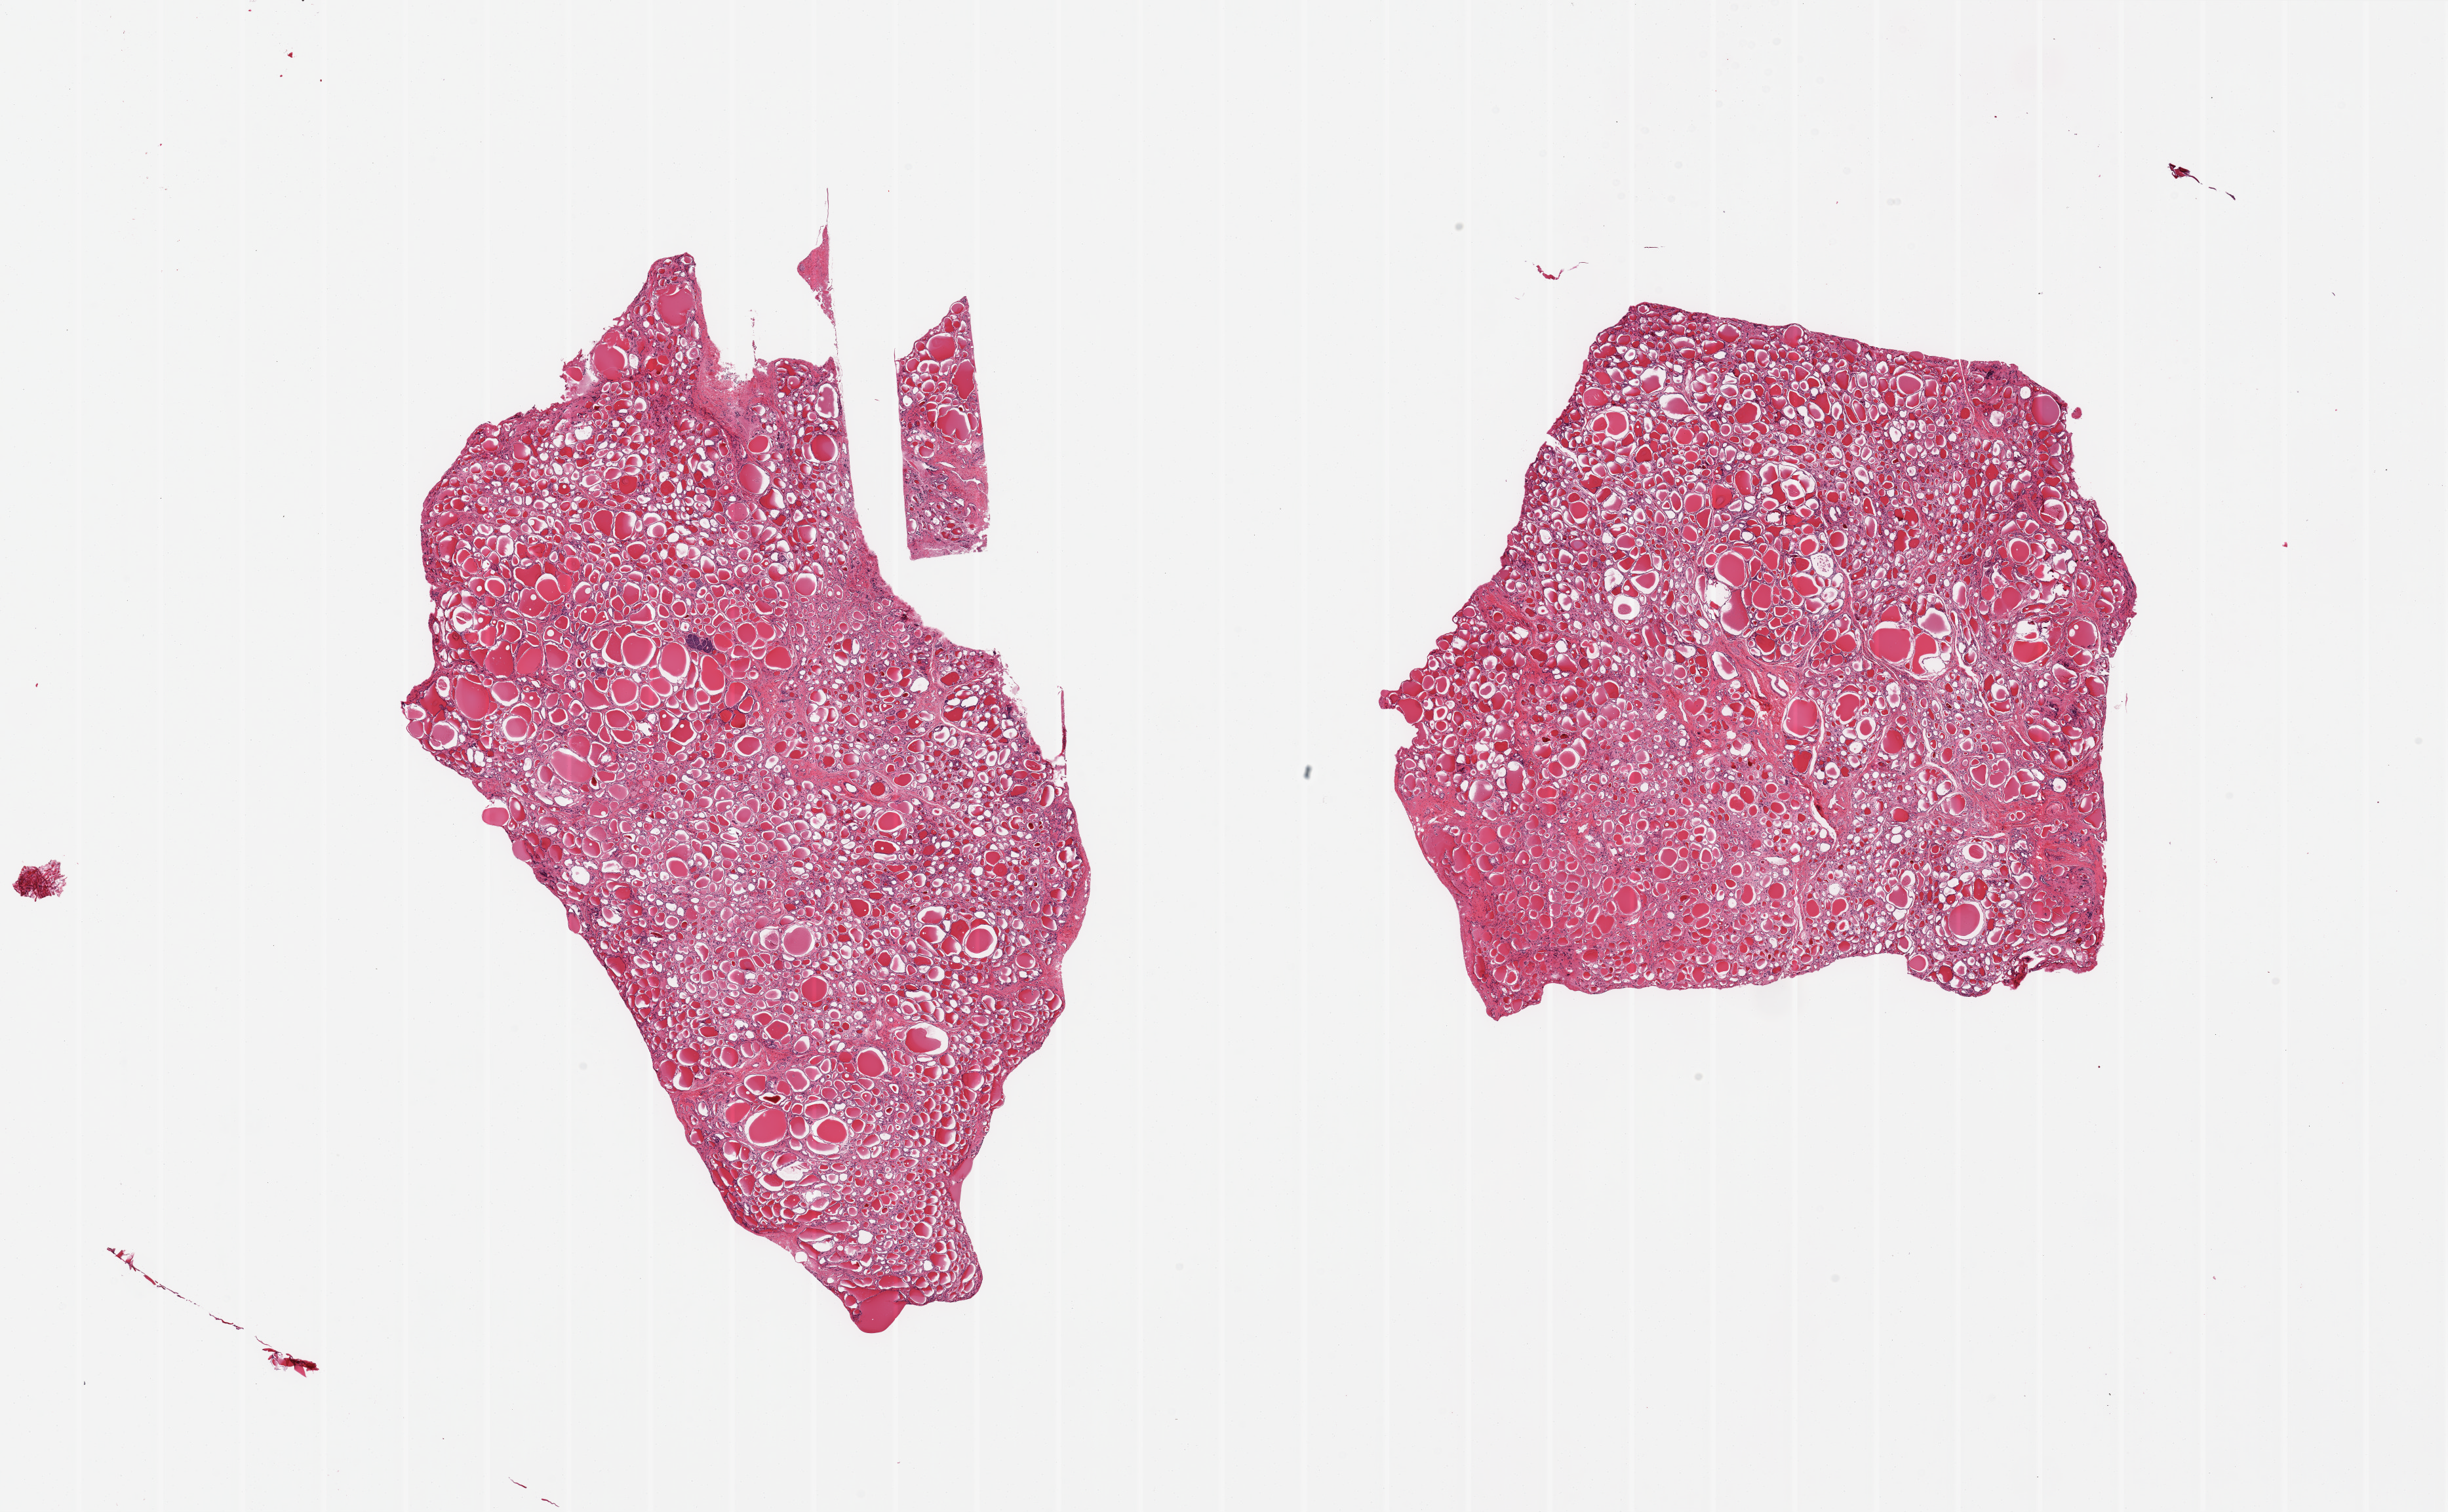
Digitized hematoxylin and eosin (H&E)-stained section — shown as a low-resolution overview of the whole scanned area (about 29.5 x 18.2 mm, from a 20x scan), PAXgene-fixed, paraffin-embedded tissue, section of thyroid (target tissue), donor tissue sample. Donor: female.
Review note (as recorded): 2 pieces; ? focal solid cell nest.